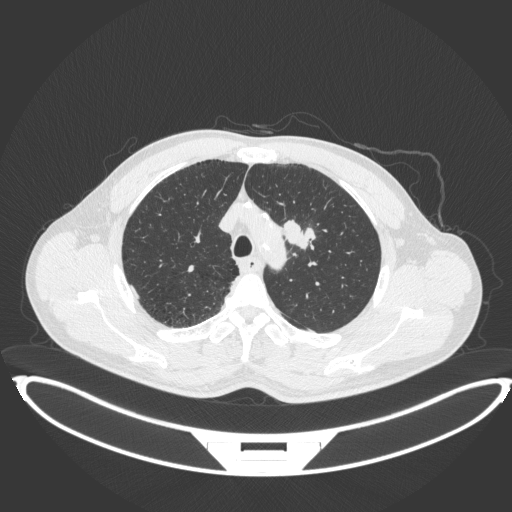
Chest CT, one axial slice. Slice 336 of 407 in the series (ordered by position). Reconstruction kernel B31f. 120 kVp. Lung window (W 1500 / L -600 HU). 1 mm slice thickness. 512 × 512 image matrix, field of view 457 × 457 mm. Male patient, age 60 years. Case-level facts recorded for this patient, not image findings: clinical TNM (as recorded): T2a N0 M0; histopathological grade: G1-G2.
Annotated regions visible in this slice (bounding box drawn by a radiologist):
- lung tumour (recorded histology: squamous cell carcinoma): bounding box (x1, y1, x2, y2) in pixels: (284, 213, 316, 251)